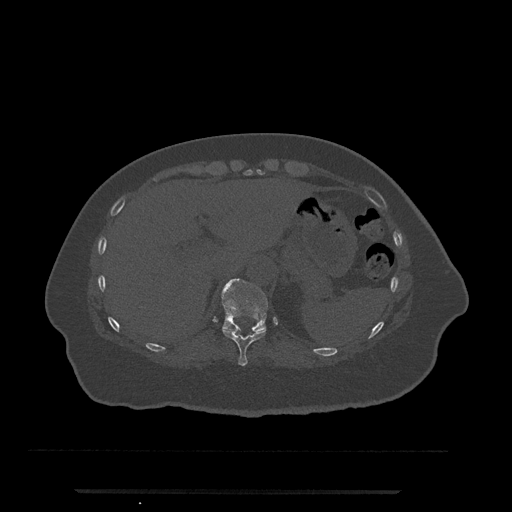
CT including the spine, one axial slice; position 259 of 797 along the scan axis; reconstruction kernel Br40s/3; bone window (W 1800 / L 400 HU); 0.5 mm slice thickness; 512 × 512 image matrix, field of view 440 × 440 mm. Female patient, age 51 years. From the clinical record (not read from this slice): primary cancer: neuro.
Structures marked on this image (semi-automatically segmented with operator editing):
- T10 vertebra: bounding box <222,328,266,366> (left, top, right, bottom; pixels)
- T11 vertebra: <222,278,268,333>